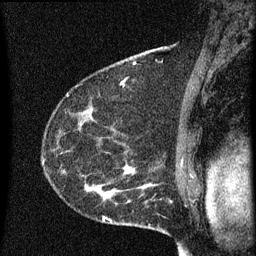
Breast MRI (dynamic contrast-enhanced), one sagittal slice; position 43 of 60 along the scan axis; dynamic contrast-enhanced series, image 2 of 3 at this slice position (ordered by acquisition); 1.5 T; TE 4.2 ms, TR 8 ms; 2 mm slice thickness; 256 × 256 image matrix, field of view 180 × 180 mm. Female patient, age 55 years.
Annotated regions visible in this slice (semi-automatically segmented with operator editing):
- analysis volume of interest (the breast-tissue region the enhancement analysis was run in; not a lesion): bounding box (x1, y1, x2, y2) in pixels: (51, 156, 145, 217)
- tumour enhancement mask (voxels above the 70 % enhancement threshold inside the analysis volume of interest): (85, 166, 145, 201)